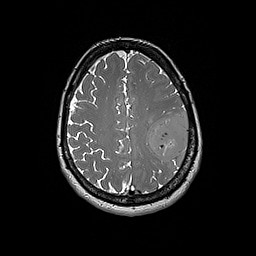
Brain MRI from a brain-tumour surgery series, one axial slice. Slice 66 of 192 in the series (ordered by position). 1 mm slice thickness. 256 × 256 image matrix, field of view 250 × 250 mm. Case-level facts recorded for this patient, not image findings: histopathology: Glioblastoma; WHO grade: 4; IDH mutation: no; tumour location: Left Frontal.
Structures marked on this image (outlined manually by an expert reader):
- tumour: bounding box (x1, y1, x2, y2) in pixels: (148, 114, 189, 167)